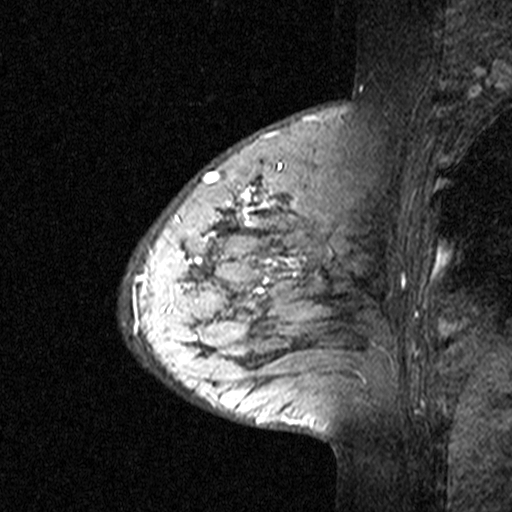
Breast MRI (dynamic contrast-enhanced), one sagittal slice; slice 12 of 44 in the series (ordered by position); dynamic contrast-enhanced study with each time point stored as its own series, time point 3 of 4 at this slice position (ordered by acquisition time); 1.5 T; TE 4.5 ms, TR 11 ms; 512 × 512 image matrix. Female patient, age 65 years. Case-level facts recorded for this patient, not image findings: setting: breast cancer imaged before/during neoadjuvant chemotherapy; receptor status: HER2-positive.
Outlined on this slice (semi-automatic segmentation, software-assisted and operator-edited):
- analysis volume of interest (the breast-tissue region the enhancement analysis was run in; not a lesion): box from (x=182, y=190) to (x=353, y=361) px
- tumour enhancement mask (voxels above the 90 % enhancement threshold inside the analysis volume of interest): (x=182, y=190)–(x=312, y=291)